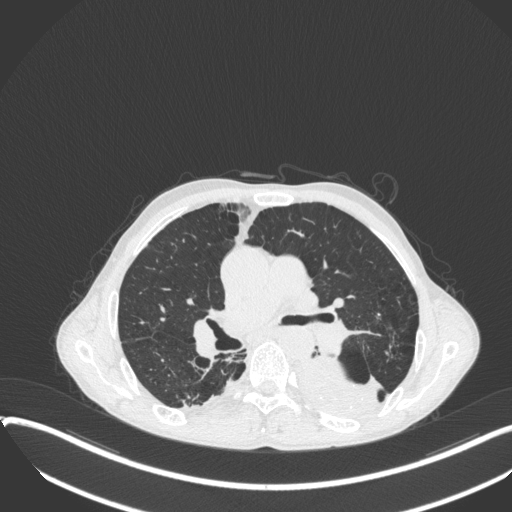
Chest CT, one axial slice. Slice 223 of 400 in the series (ordered by position). 120 kVp. Lung window (W 1500 / L -600 HU). 1 mm slice thickness. 512 × 512 image matrix, field of view 400 × 400 mm. Male patient, age 57 years. Case-level facts recorded for this patient, not image findings: clinical TNM (as recorded): T4 N0 M0.
Outlined on this slice (rectangle marked by the reading radiologist):
- lung tumour (recorded histology: squamous cell carcinoma): bounding box <291,346,387,420> (left, top, right, bottom; pixels)